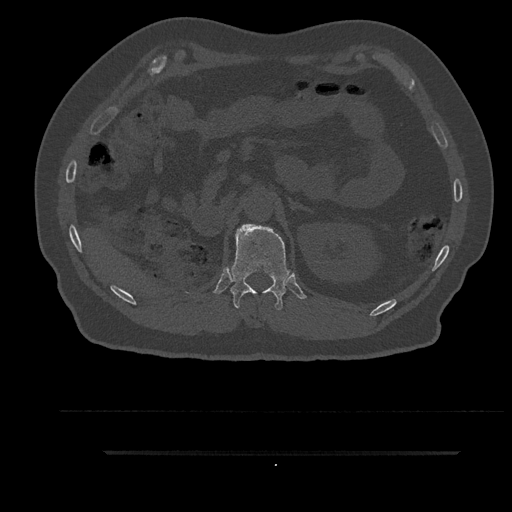
CT including the spine, one axial slice. Position 245 of 797 along the scan axis. Reconstruction kernel Br40s/3. 120 kVp. Bone window (W 1800 / L 400 HU). 0.5 mm slice thickness. 512 × 512 image matrix, field of view 432 × 432 mm. Male patient, age 63 years. Case-level facts recorded for this patient, not image findings: primary cancer: renal; vertebrae with lytic lesions (as recorded): T8.
Structures marked on this image (semi-automatically segmented with operator editing):
- T12 vertebra: bounding box [x1, y1, x2, y2] px = [229, 224, 290, 310]